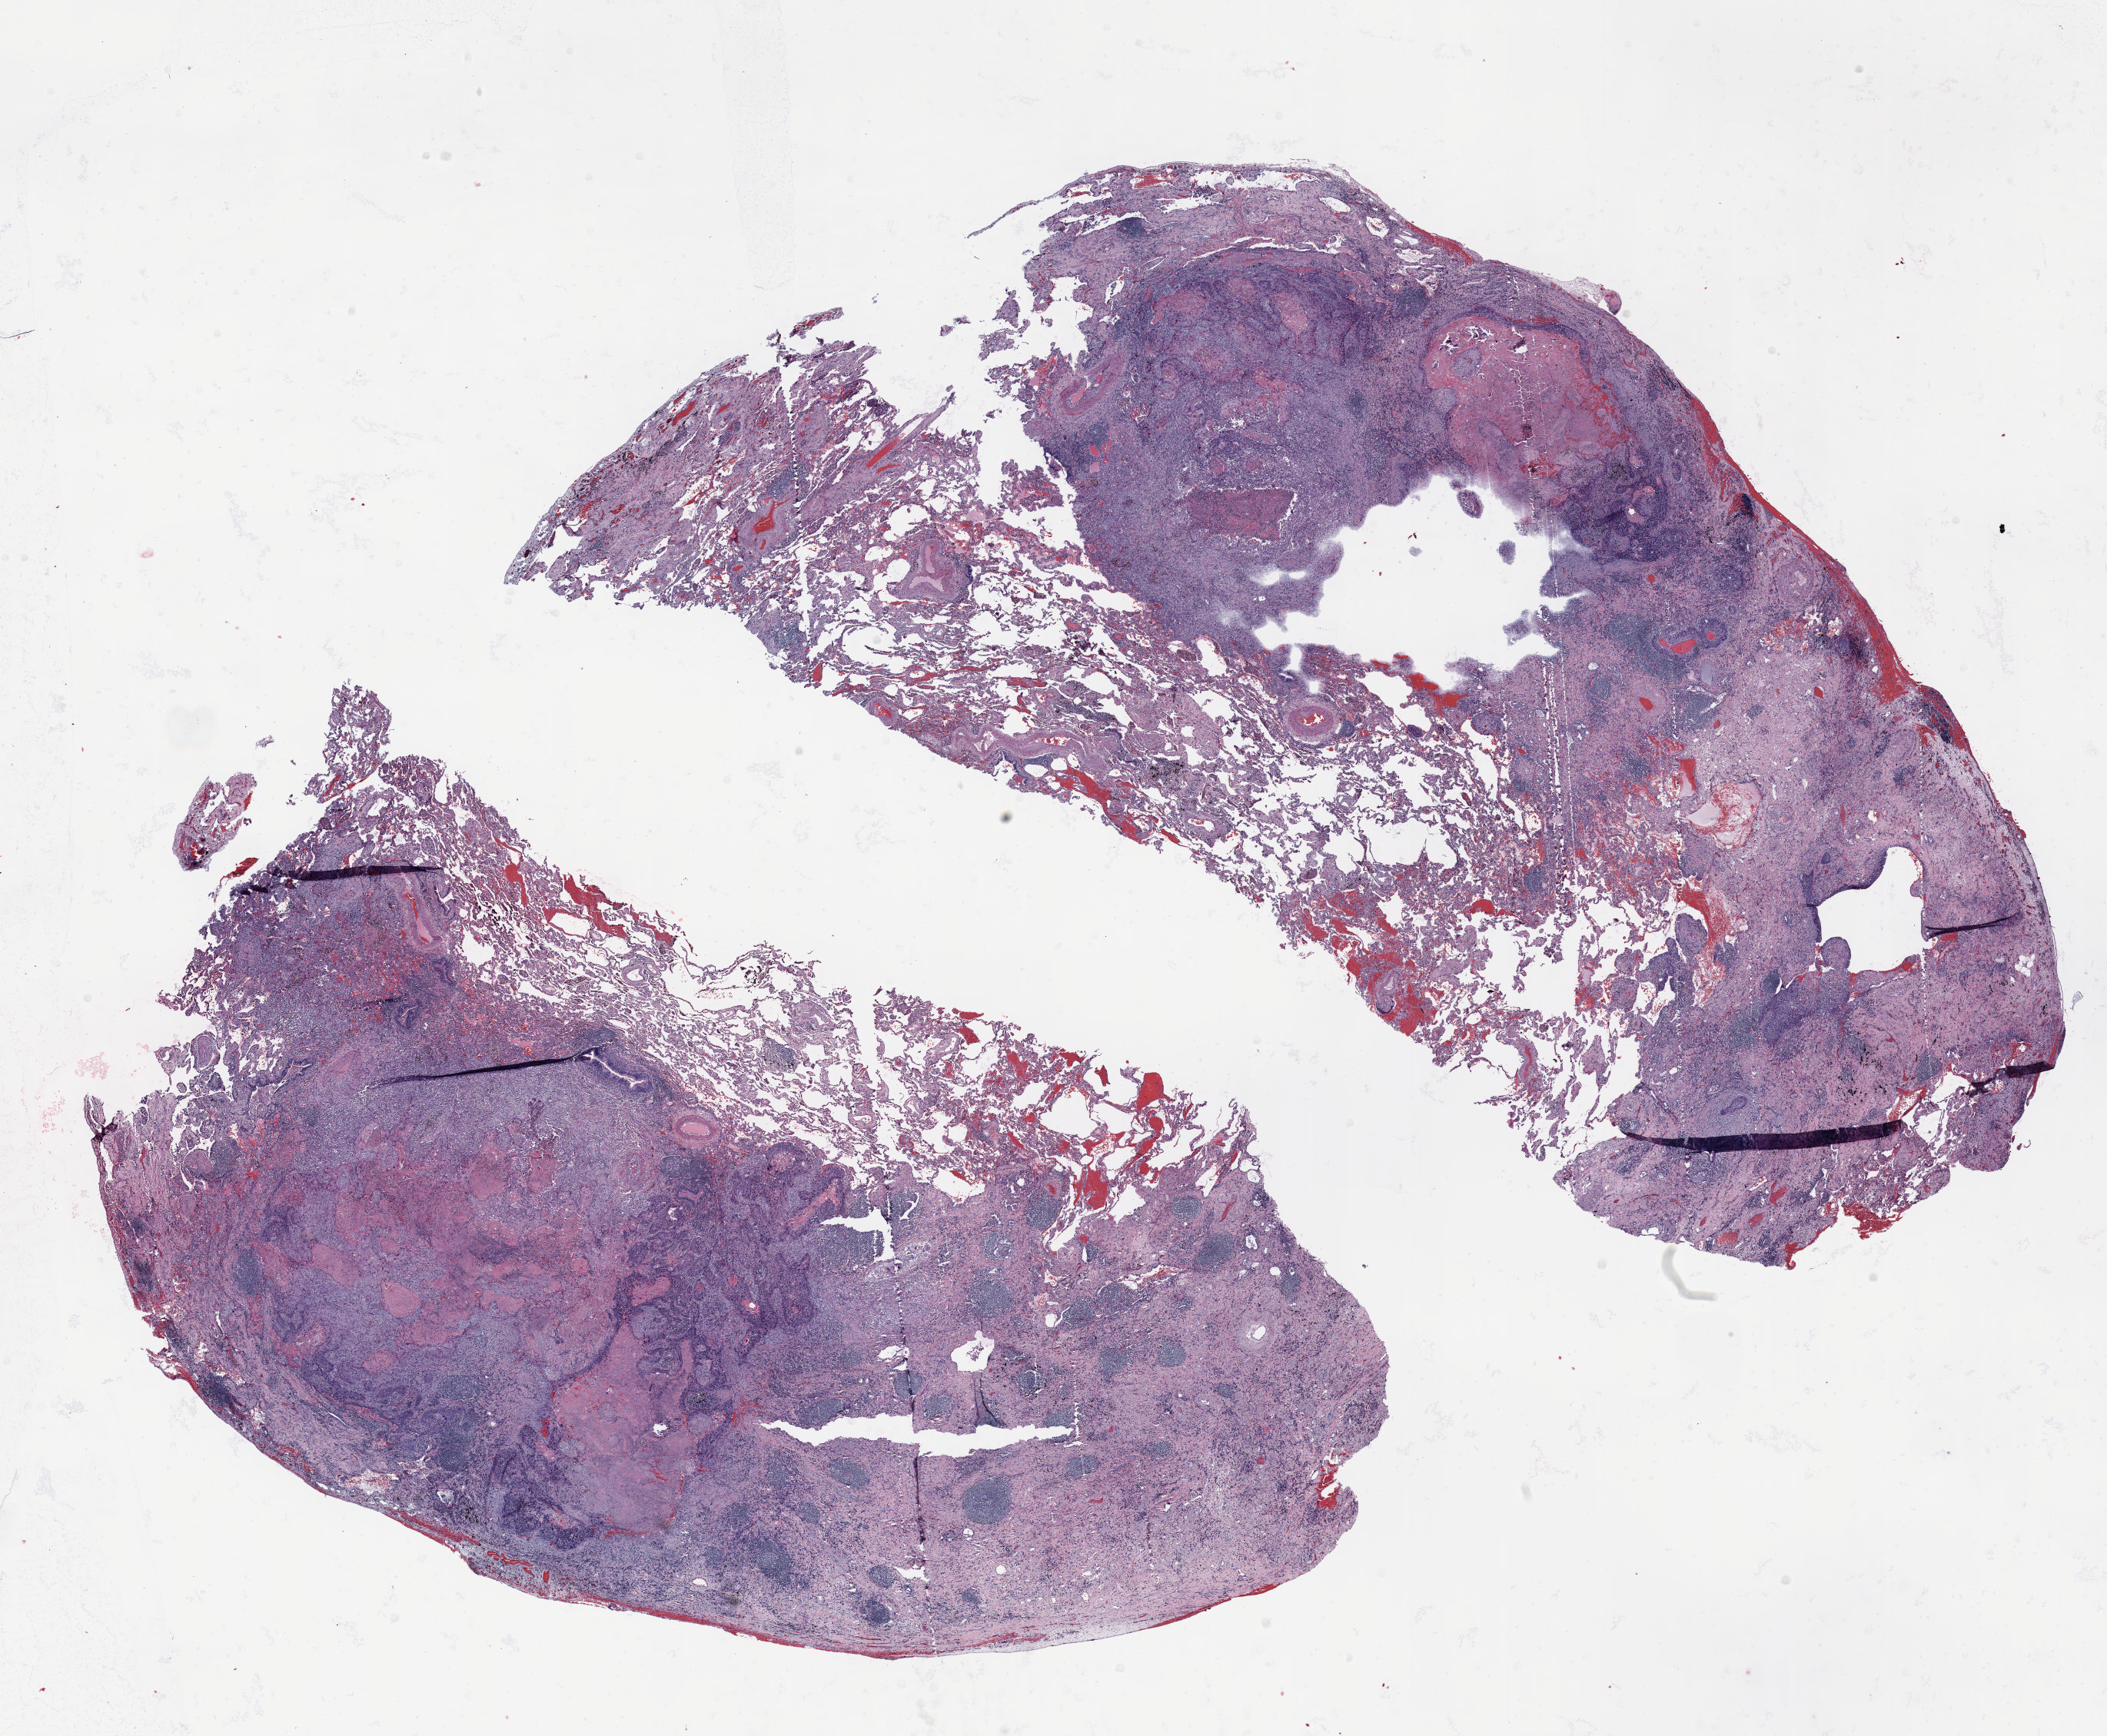
Whole-slide histology image, Hematoxylin and eosin (H&E) stained, low-resolution overview of the scanned area, about 22.0 x 18.1 mm (from a 20x scan). FFPE section. Lung. Female, age 70 at enrolment. Grade: well differentiated (G1).
Stage (AJCC 6th edition): IA. Tumour size (pathology): 25 mm. Participant's lung-cancer diagnosis: Squamous cell carcinoma, NOS. Primary tumour location (clinical record): right lower lobe.